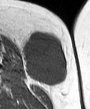
MRI of an extremity soft-tissue mass, one axial slice; position 16 of 45 along the scan axis; MR volume resampled by the dataset authors to the PET/CT grid (not the native acquisition matrix); 3.27 mm slice thickness; 90 × 109 image matrix. Female patient. Case-level facts recorded for this patient, not image findings: histological type: leiomyosarcoma; grade: intermediate; site of the primary tumour: parascapusular.
Annotated regions visible in this slice (expert contour drawn on MRI and transferred to this co-registered scan by the dataset authors):
- gross tumour volume including surrounding oedema: bounding box <23,32,68,86> (left, top, right, bottom; pixels)
- gross tumour volume (mass): <23,32,68,86>